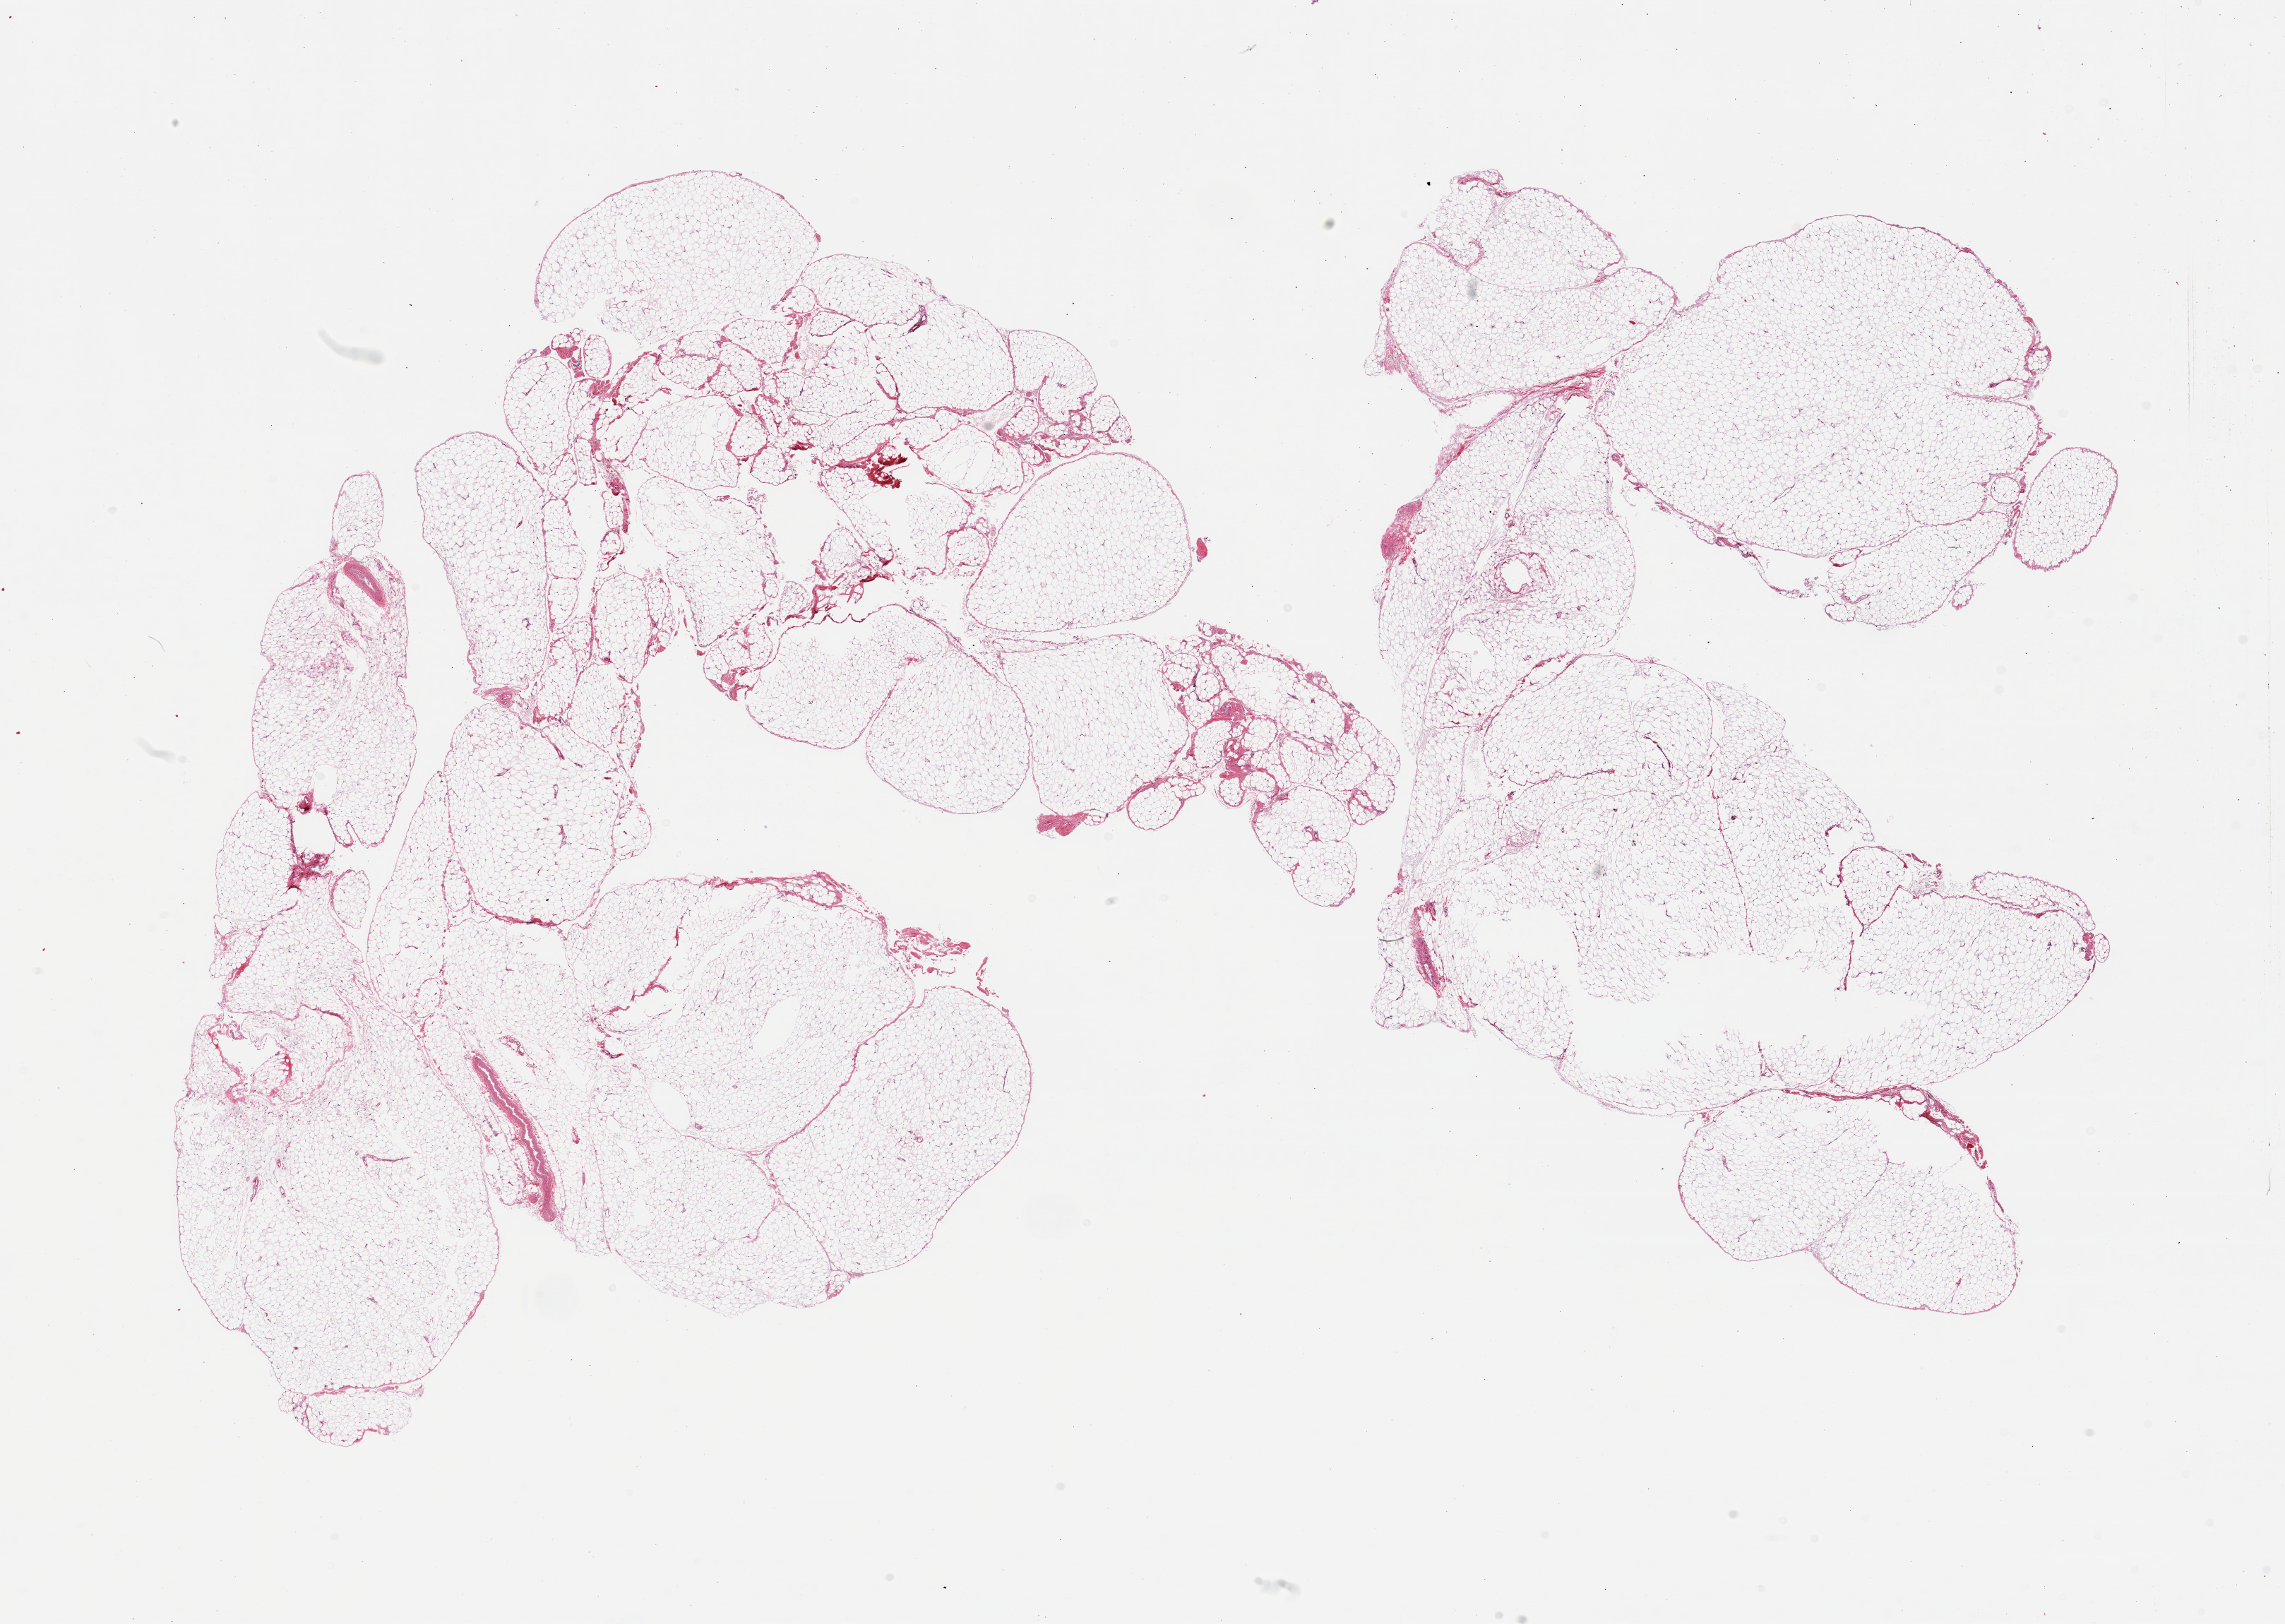
Haematoxylin and eosin whole-slide image, whole scanned area (about 25.6 x 18.2 mm, from a 20x scan) shown as a low-resolution overview; PAXgene-fixed paraffin-embedded (PFPE) section; sampled site (target tissue): omentum; tissue donor sample. Male donor.
Review note (as recorded): 2 pieces; mature adipose tissue.